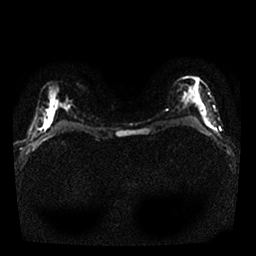
Breast MRI, one axial slice. Position 14 of 25 along the scan axis. Diffusion-weighted series; image 2 of 4 stored at this slice position (different b-values; order by instance number). 1.5 T. 4 mm slice thickness. 256 × 256 image matrix, field of view 320 × 320 mm. Female patient.
Structures marked on this image (expert manual segmentation):
- tumour on diffusion-weighted imaging: bounding box [x1, y1, x2, y2] px = [202, 109, 209, 125]